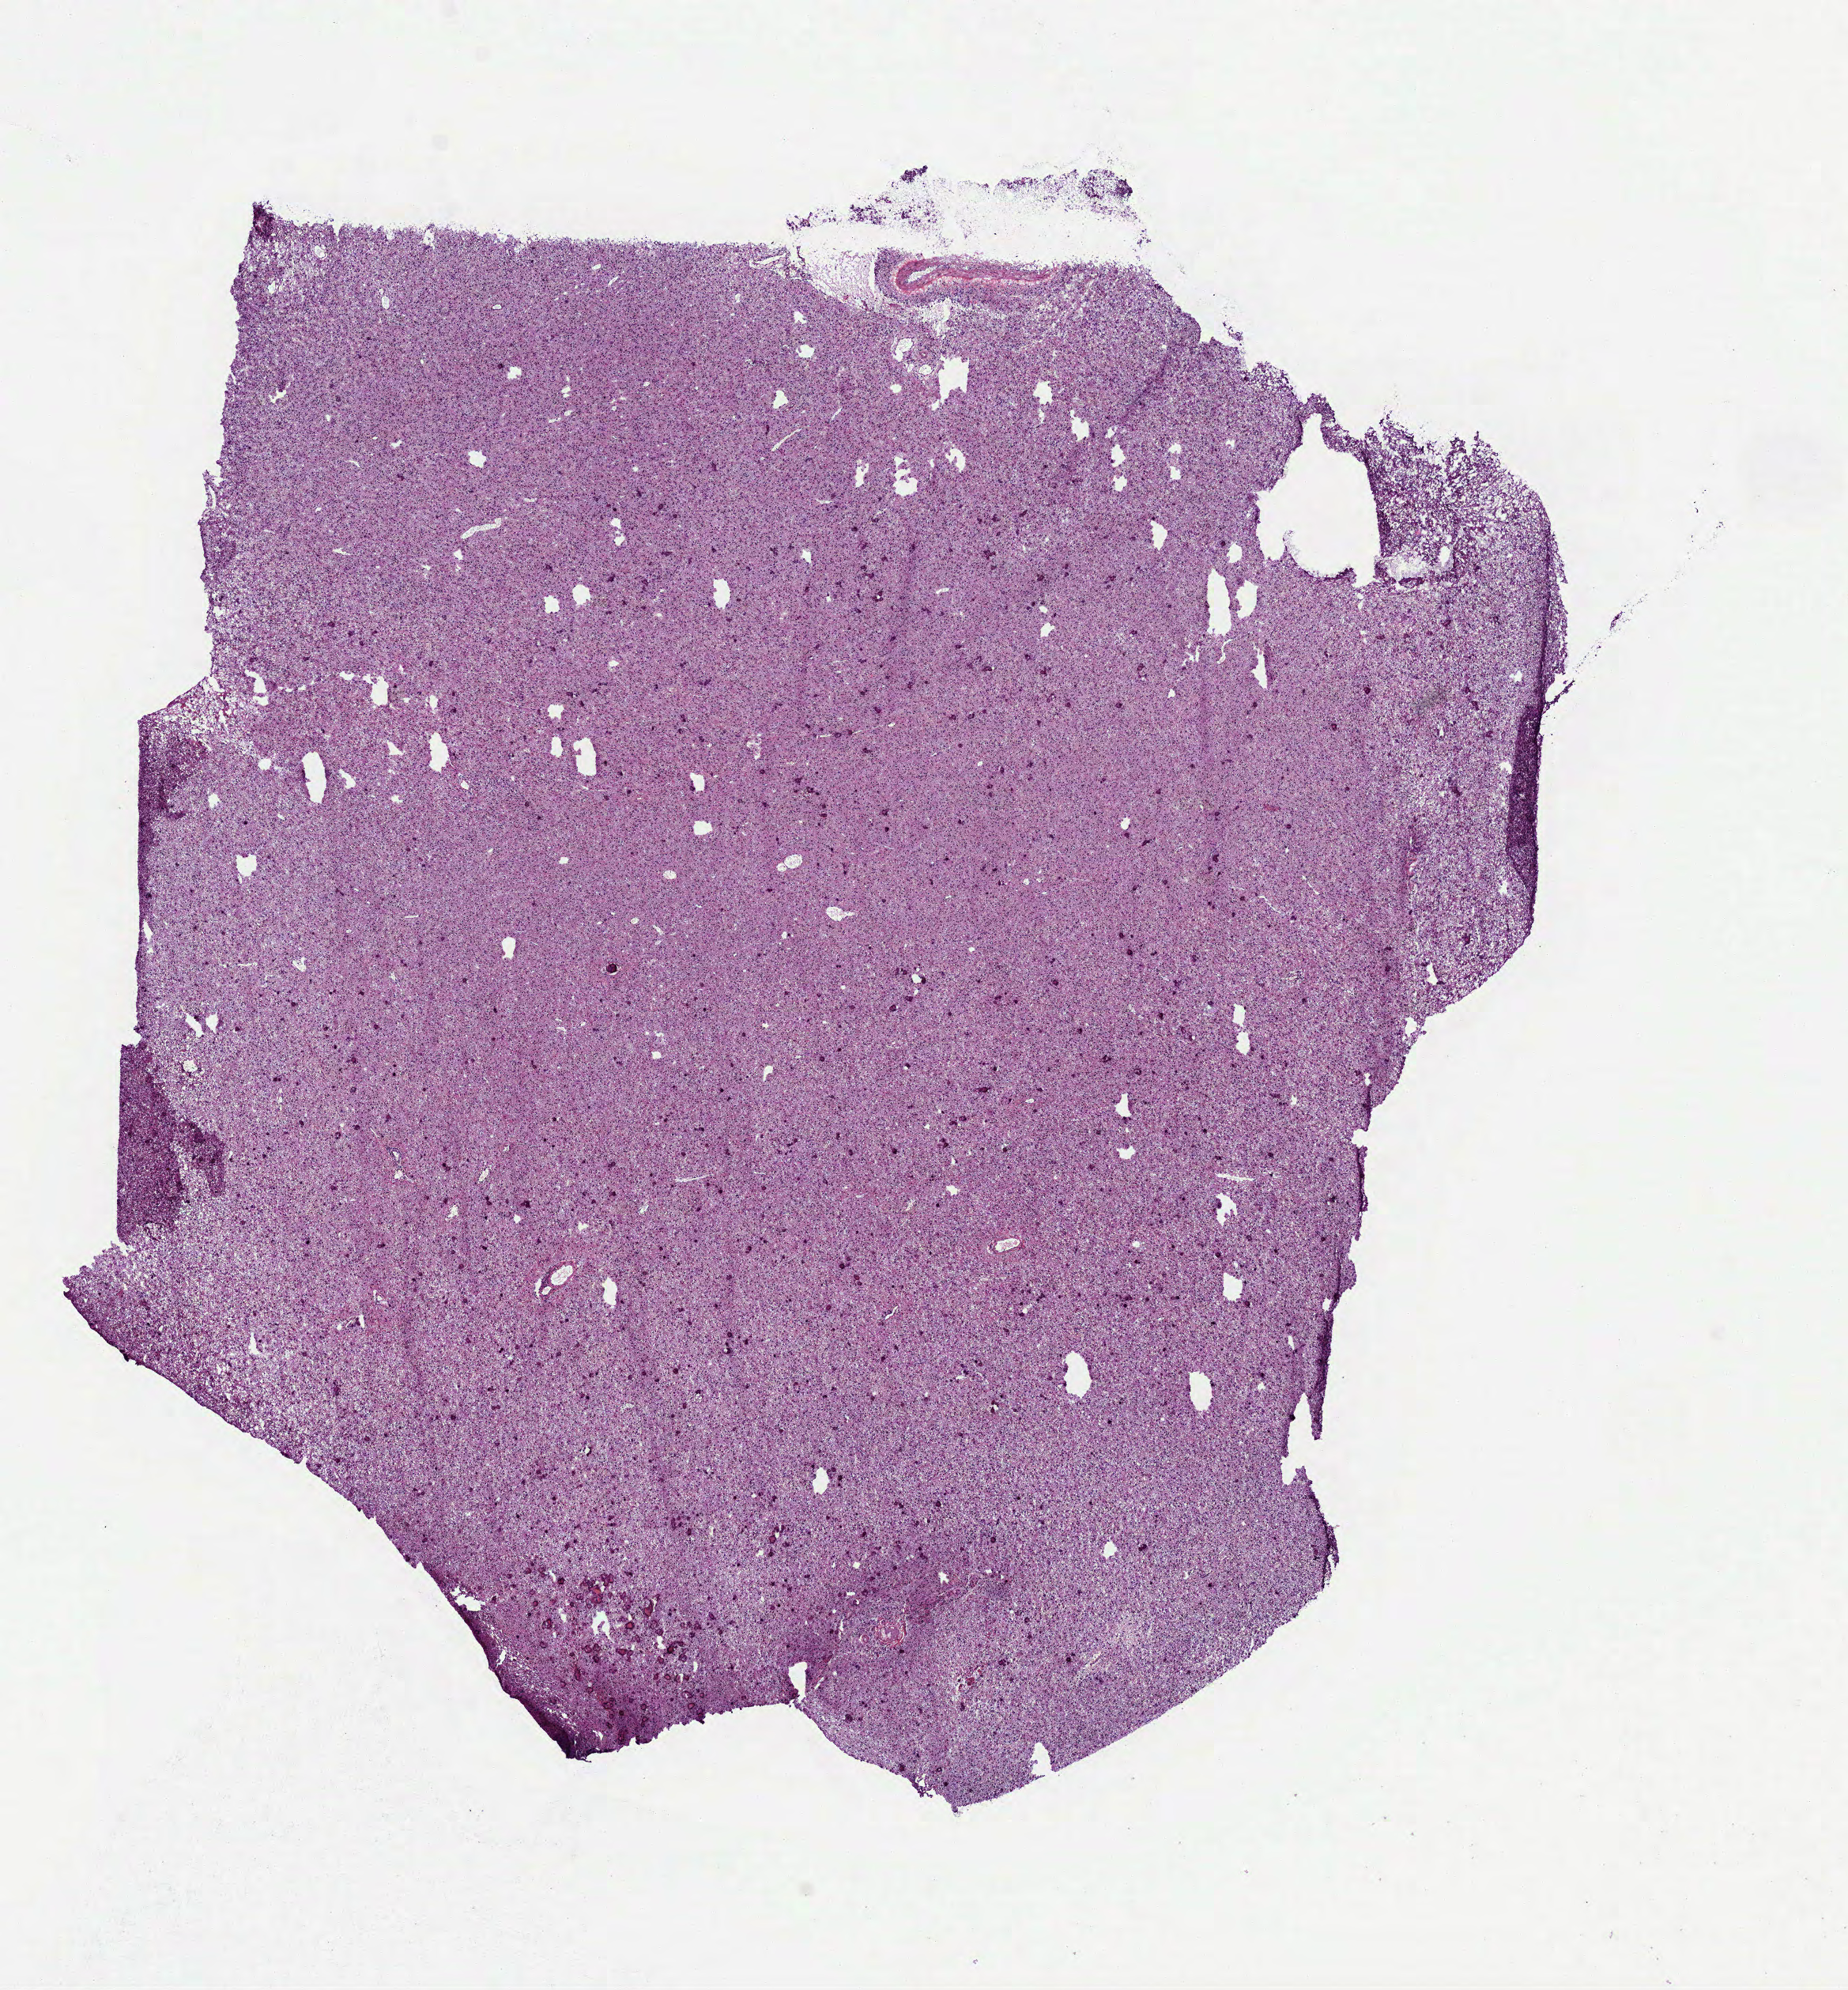
Whole-slide histology image, Hematoxylin and eosin (H&E) stained — low-resolution overview of the scanned area, about 9.4 x 10.1 mm. Frozen section from the top of the tissue portion. Primary tumour sample from the brain. Patient: female, age at initial diagnosis 60 years. Histologic grade: G3 (poorly differentiated). Pathologist review of this section (percent, as recorded): tumour cells 100%, tumour nuclei 80%, normal cells 0%, stromal cells 0%, necrosis 0%.
Diagnosis: Astrocytoma, anaplastic.